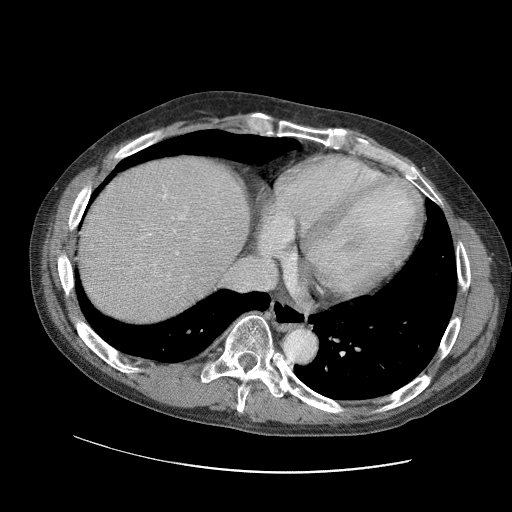
Contrast-enhanced abdominal CT (liver protocol), one axial slice. Position 88 of 109 along the scan axis. 120 kVp. Soft-tissue window (W 400 / L 40 HU). 2.5 mm slice thickness. 512 × 512 image matrix. From the clinical record (not read from this slice): diagnosis: hepatocellular carcinoma (patient treated with transarterial chemoembolisation; whether this scan precedes or follows treatment is not stated here); TNM stage (as recorded): Stage-IIIC; Child-Pugh class: B; tumour differentiation: well differentiated.
Outlined on this slice (semi-automatically segmented with operator editing):
- liver parenchyma outside the tumour (the mass and vessels are separate outlines, so this box may not span the whole liver): bounding box [x1, y1, x2, y2] px = [76, 154, 248, 322]
- liver vessels: [127, 185, 218, 290]